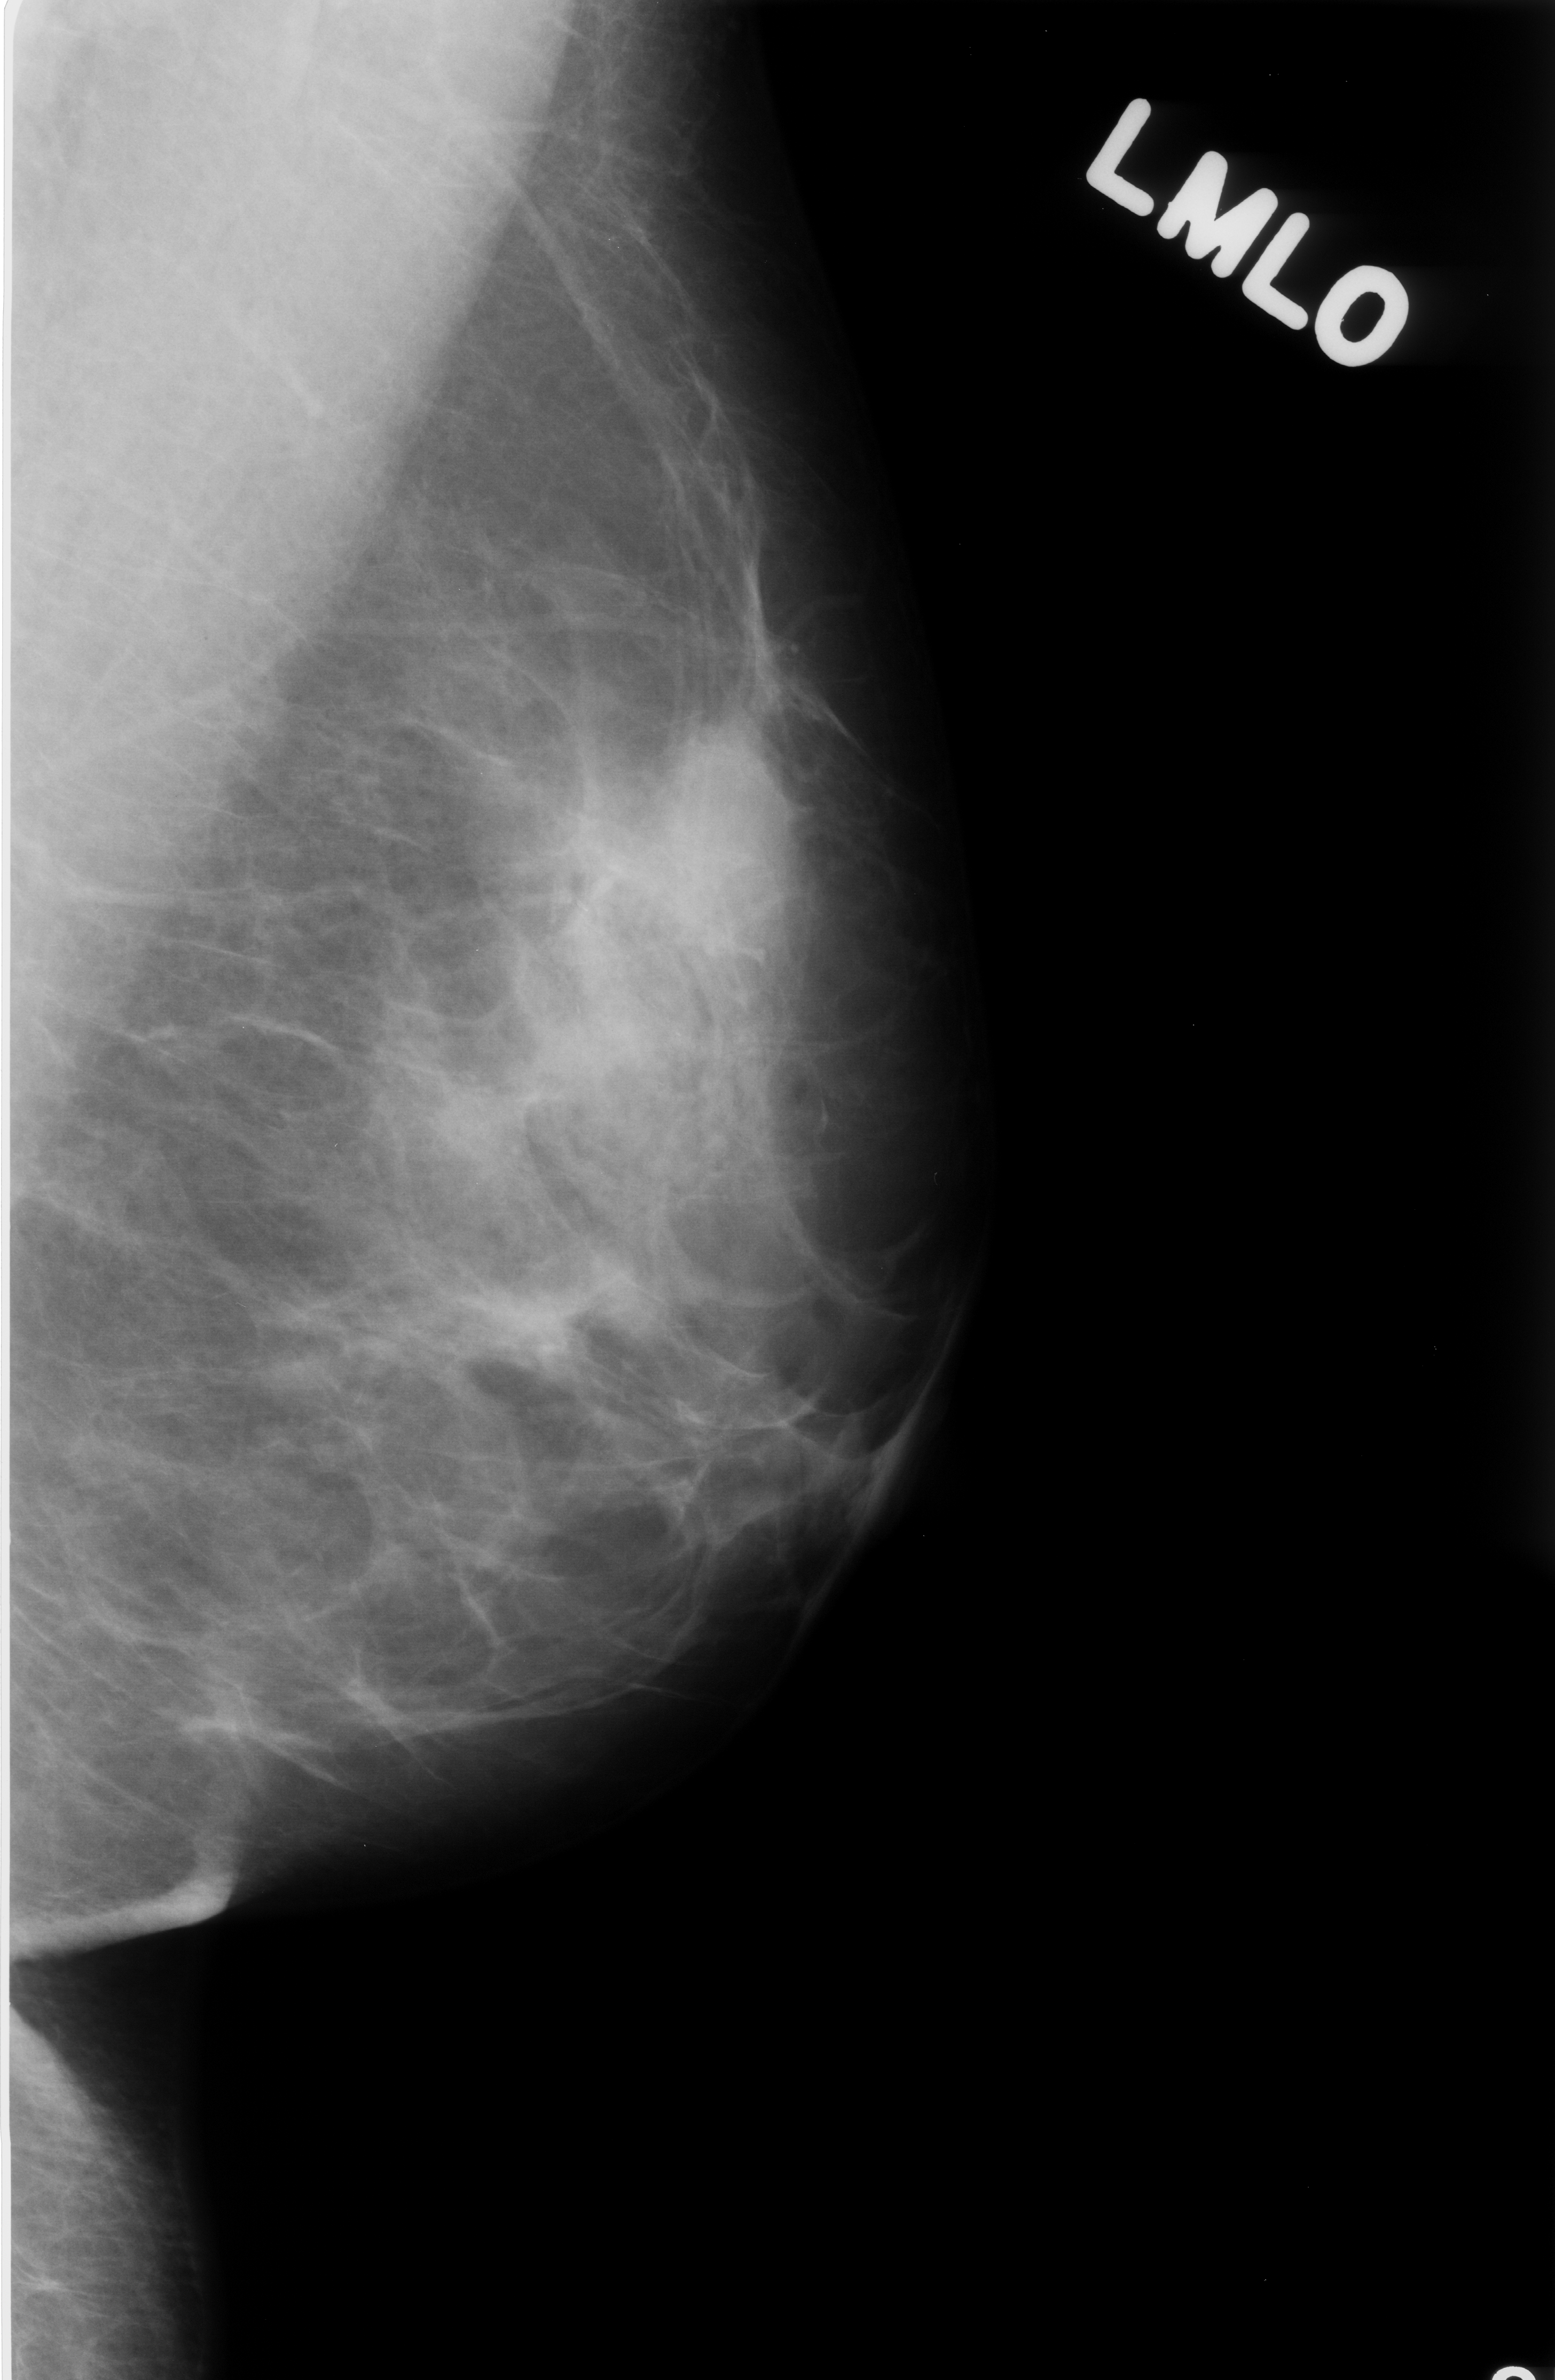
Mammogram (digitized film); left breast; mediolateral oblique (MLO) view; BI-RADS breast density category 2 (scale 1–4); 1555 × 2380 image matrix.
Expert-marked regions of interest on this image (one box per marked abnormality):
- calcifications, morphology fine linear branching, distribution linear; BI-RADS assessment category 4; subtlety rating 4 on a 1 (subtle) to 5 (obvious) scale; pathology (as recorded): benign: bounding box [x1, y1, x2, y2] px = [465, 717, 706, 1146]